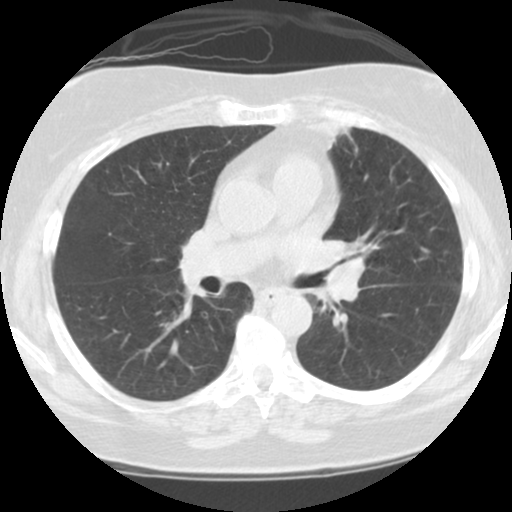
Low-dose screening chest CT, axial slice, third screening round (two years after baseline), lung window (W 1500 / L -600 HU), 2.5 mm slice thickness, standard (soft-tissue) reconstruction kernel (STANDARD), 512 × 512 image matrix. Female participant, aged 59 years at enrolment. Current smoker at enrolment.
Expert-annotated lung lesion, box from (x=285, y=213) to (x=389, y=325) px. Screening reader's record for this exam: no non-calcified nodule ≥4 mm recorded. Participant outcome: lung cancer diagnosed 192 days after this screen — small cell carcinoma, NOS, left upper lobe, left hilum, mediastinum, left main stem bronchus, stage IV (AJCC 6th edition), 63 mm at pathology.